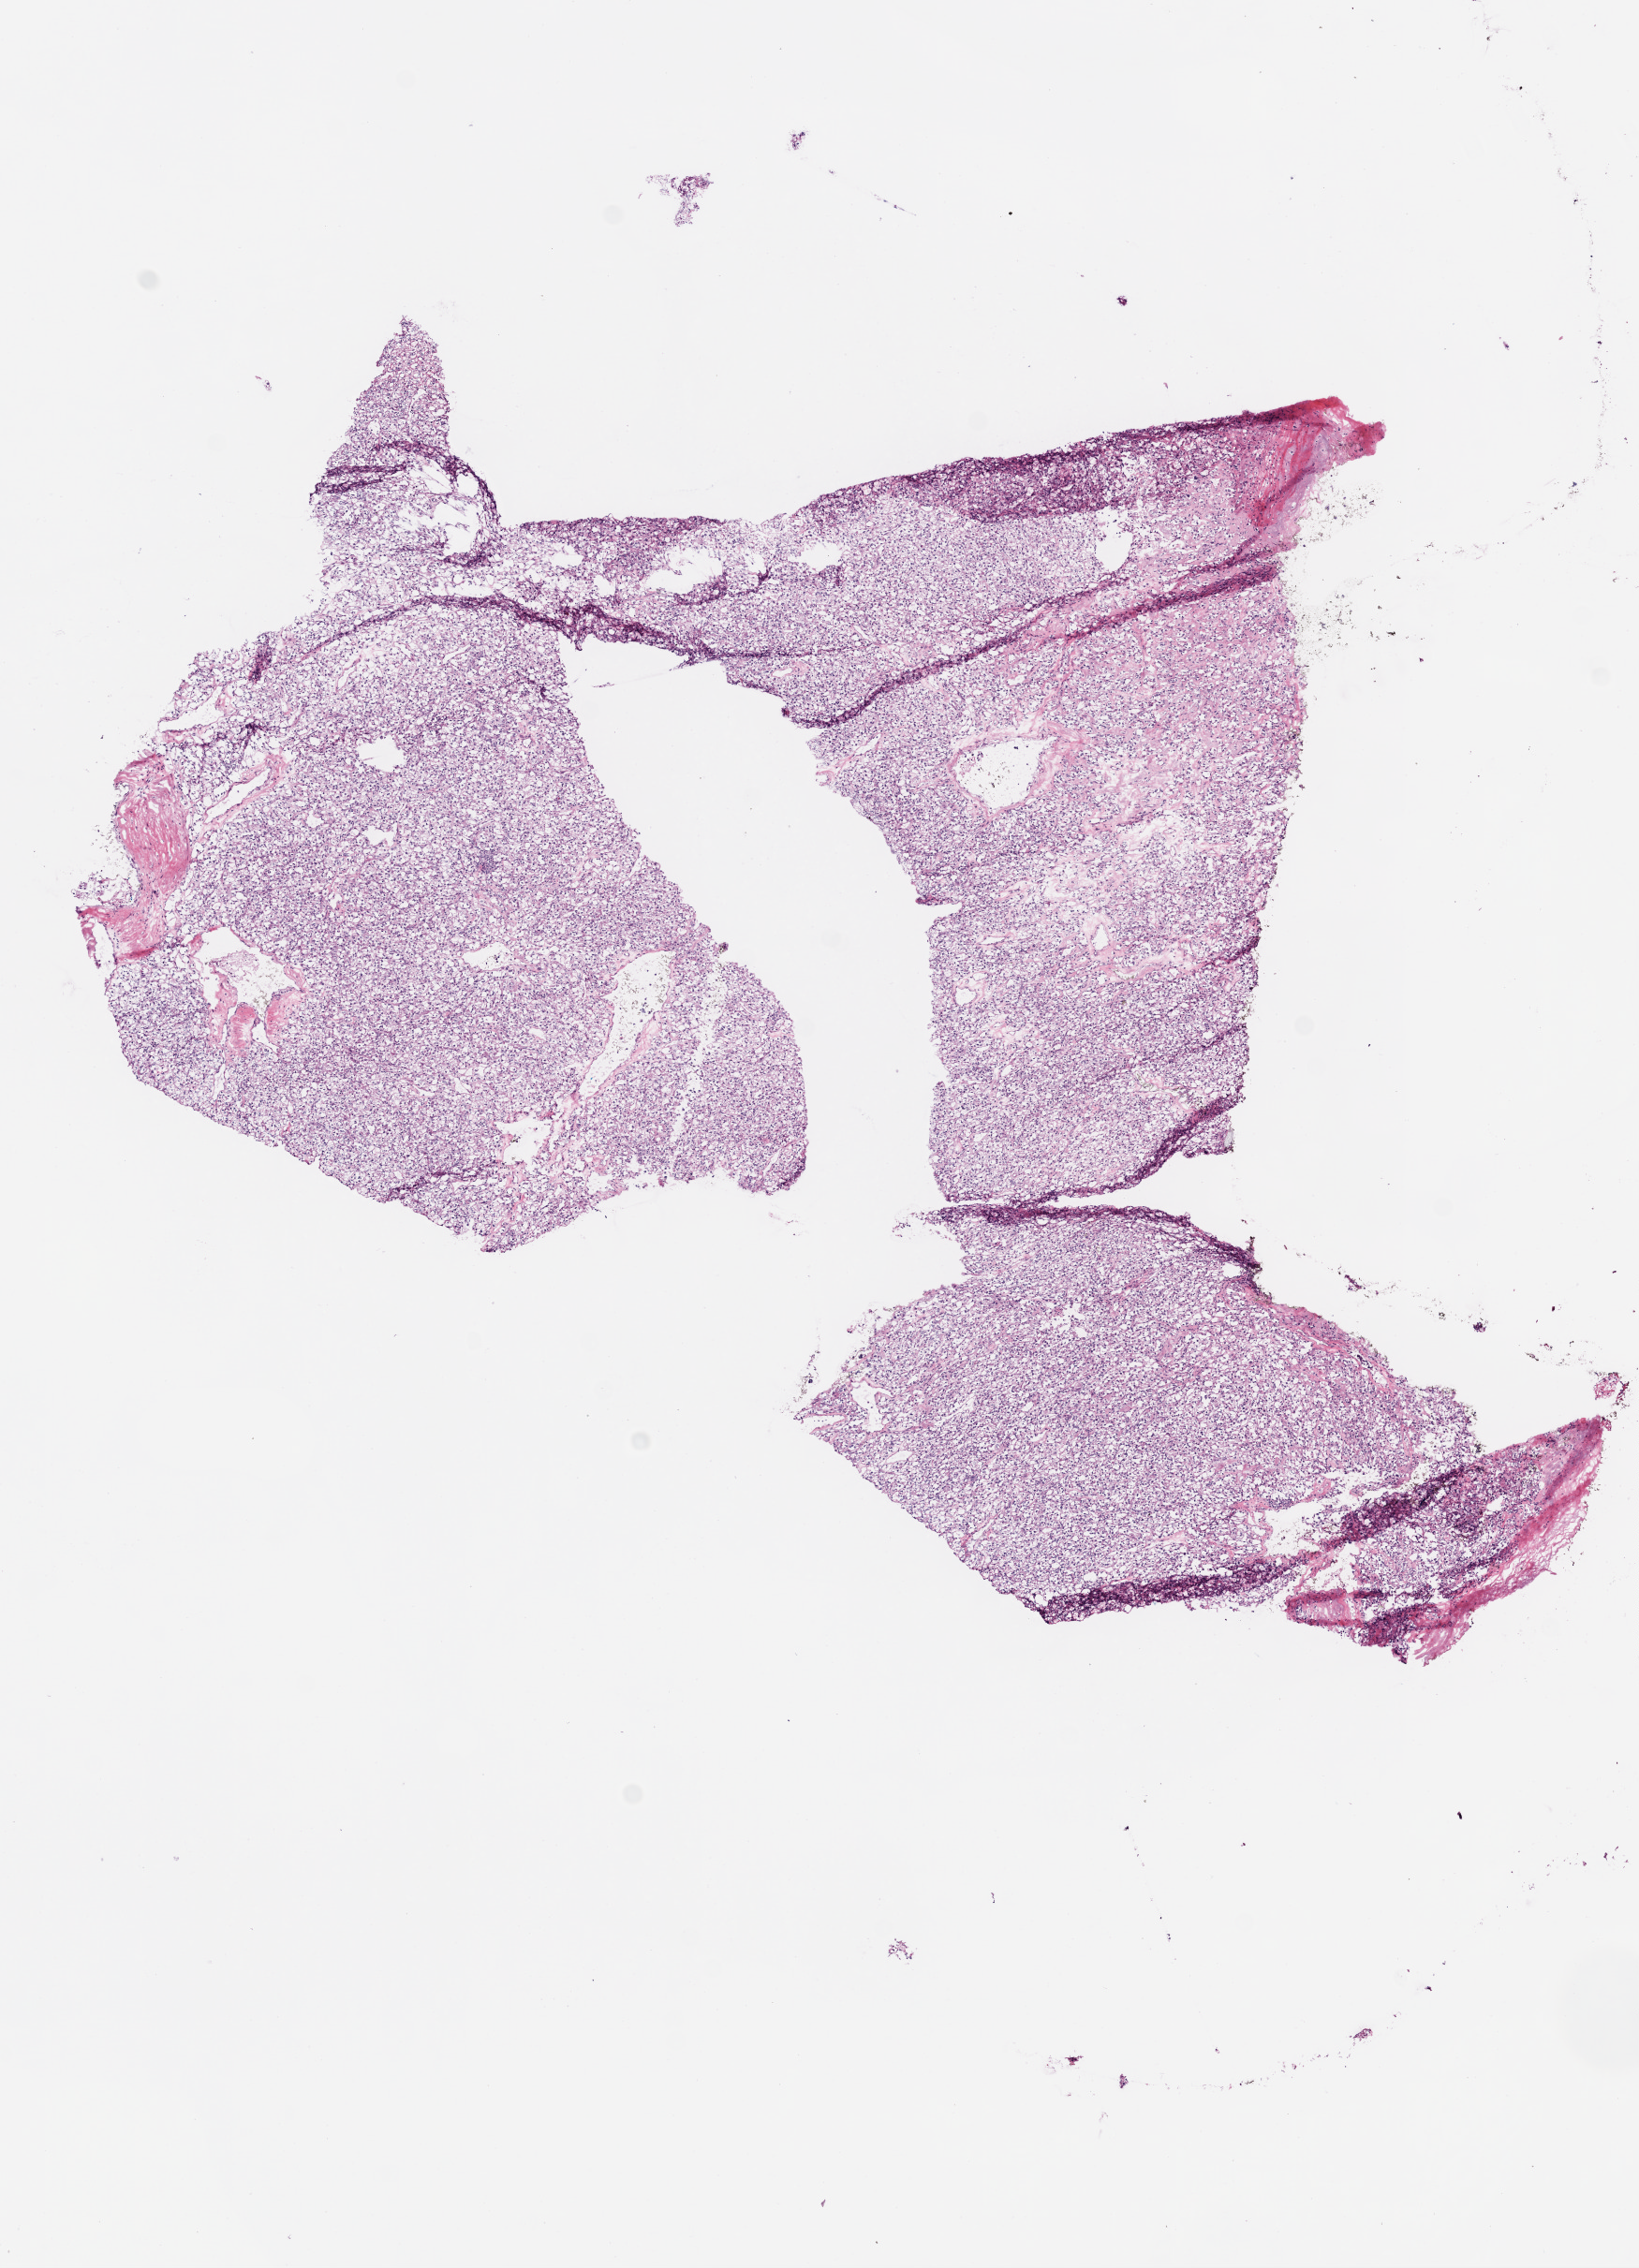
H&E-stained whole-slide image — a low-resolution overview of the entire scanned area, about 7.0 x 9.7 mm, frozen section from the bottom of the tissue portion, primary tumour sample from the kidney. Male, age 74 years at initial diagnosis. Histologic grade: G3 (poorly differentiated). Slide review estimates, as recorded: tumour cells 95%, tumour nuclei 85%, normal cells 0%, stromal cells 5%, necrosis 0%.
Diagnosis: Clear cell adenocarcinoma, NOS. Laterality: left. AJCC pathologic stage: III.